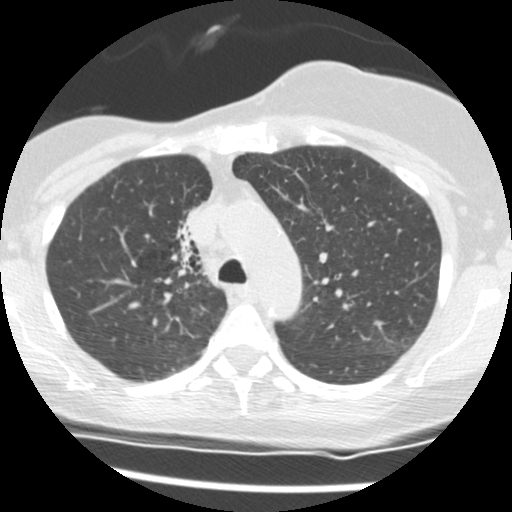
Axial slice from a low-dose chest CT screening exam, second screening round (one year after baseline), lung window (W 1500 / L -600 HU), 2.5 mm slice thickness, standard (soft-tissue) reconstruction kernel (STANDARD), 120 kVp, slice 38 of 165 in the series. Female, age 56 years at enrolment. Current smoker at enrolment.
Expert reader's lesion annotation, bounding box [x1, y1, x2, y2] px = [154, 199, 213, 277]. The screening reader recorded 2 non-calcified nodules or masses ≥4 mm on this exam; which of them this box marks is not recorded. Lung cancer was diagnosed 675 days after this screen (after the third annual screen): adenocarcinoma, NOS, right upper lobe, stage IIIB (AJCC 6th edition), 8 mm at pathology.